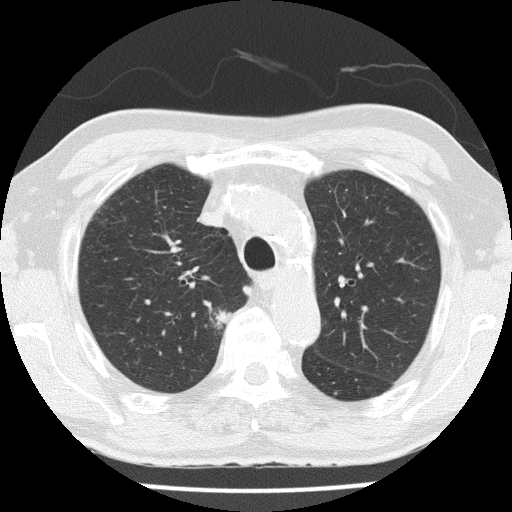
Low-dose screening chest CT, axial slice; third annual screen; lung window (W 1500 / L -600 HU); lung (sharp) reconstruction kernel (FC51); 120 kVp; slice 45 of 153 in the series; 512 × 512 image matrix. Male, age 72 years at enrolment.
• Expert-annotated lung lesion, bounding box [x1, y1, x2, y2] px = [188, 294, 242, 347].
• The exam's reader record, not a measurement of the box and not confirmed to be the same lesion: non-calcified nodule or mass ≥4 mm, right upper lobe, 14 × 14 mm, spiculated (stellate) margins, soft tissue attenuation, pre-existing on the prior screen: yes; interval growth: yes.
• Official screen result: positive, other.
• Participant outcome: lung cancer diagnosed 67 days after this screen — squamous cell carcinoma, NOS, right upper lobe, moderately differentiated (G2), stage IIA (AJCC 6th edition), 25 mm at pathology.